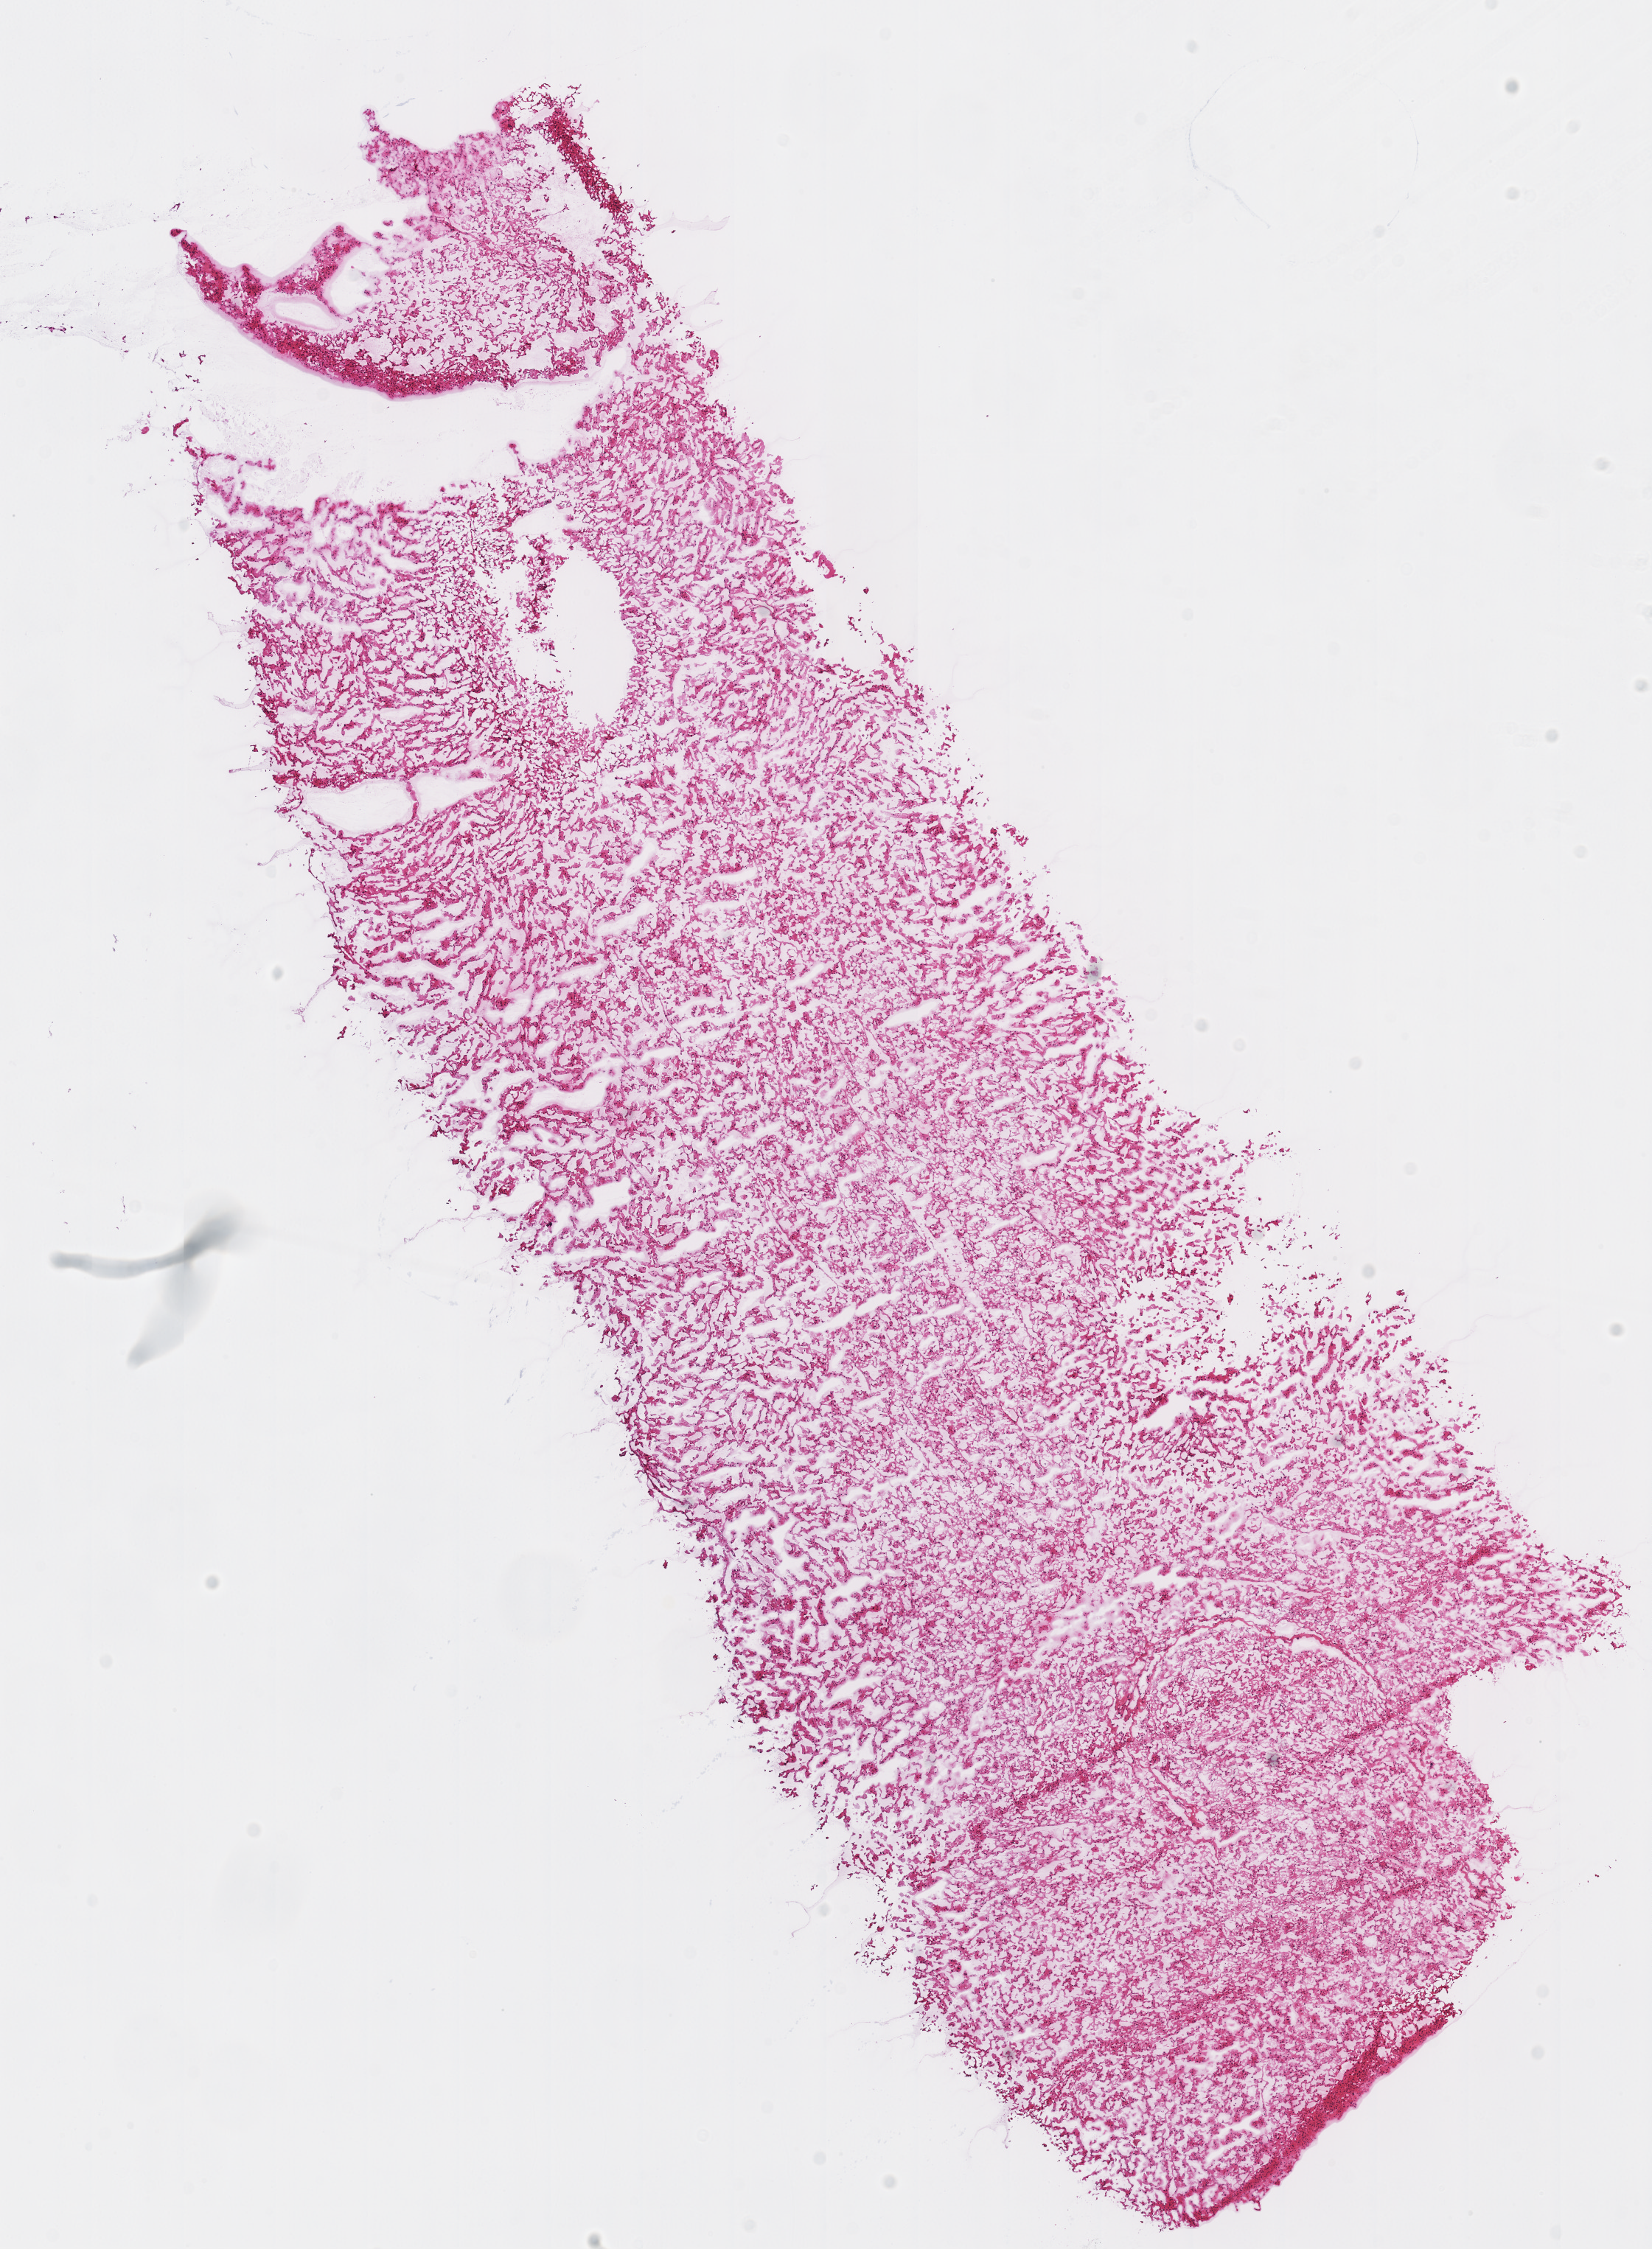
Digitized Hematoxylin and eosin (H&E) stained tissue section (whole slide), low-resolution overview of the scanned area, about 8.8 x 12.0 mm; frozen section from the top of the tissue portion; kidney, primary tumour sample. Male patient; age at initial diagnosis 58 years. Pathologist review of this section (percent, as recorded): tumour cells 90%, tumour nuclei 90%, normal cells 0%, stromal cells 10%, necrosis 0%.
TNM: T1b NX M0. AJCC pathologic stage: I (7th edition). Pathologic diagnosis: Renal cell carcinoma, chromophobe type.